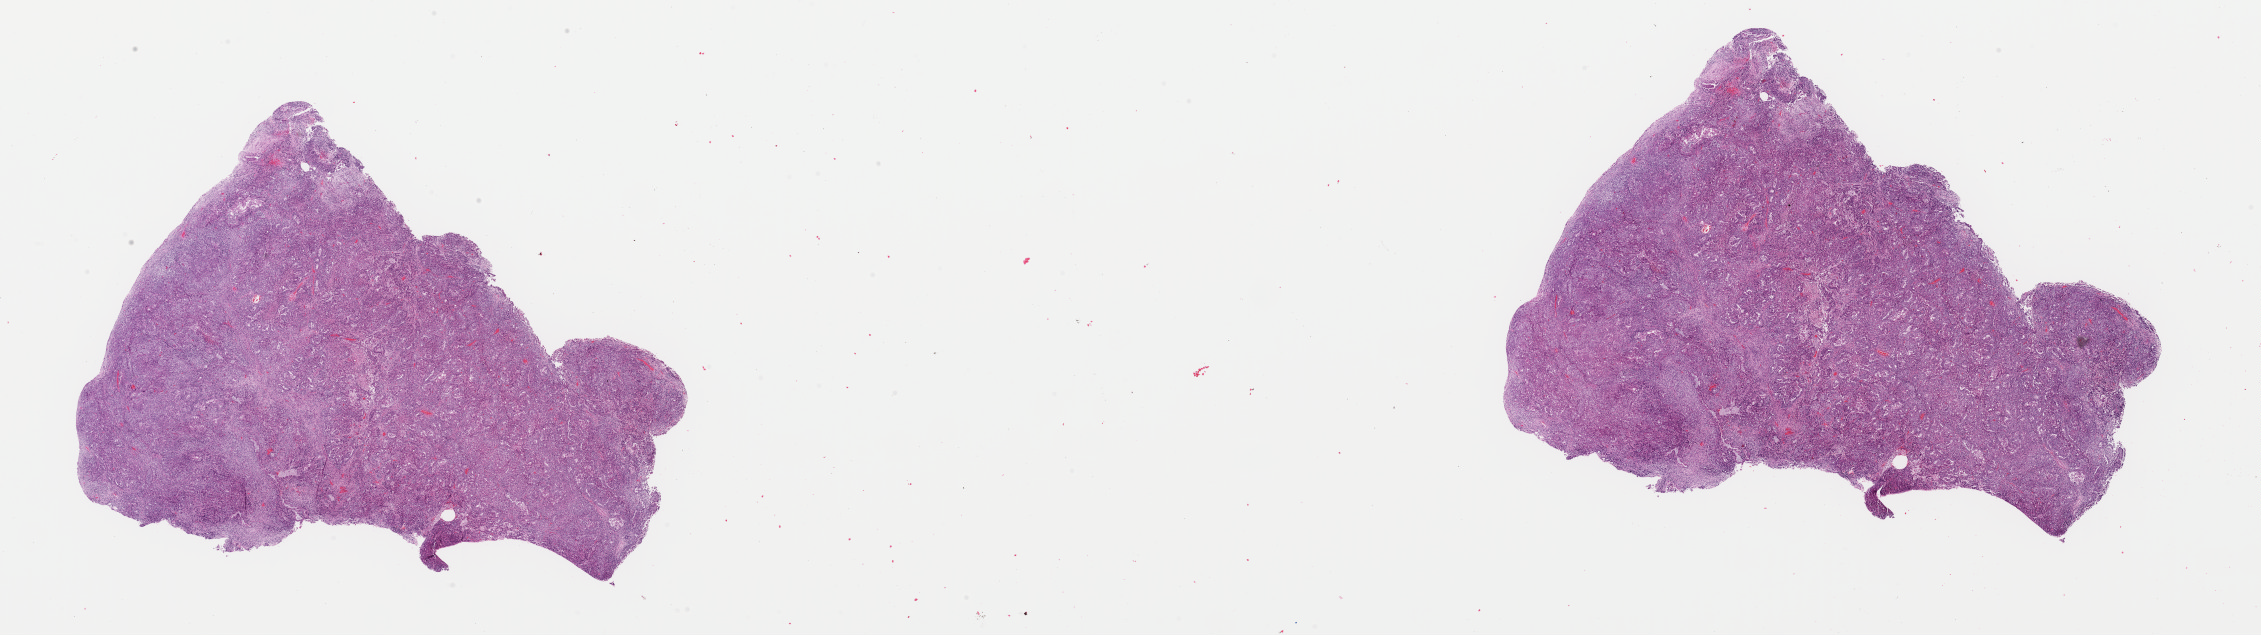
Whole-slide histology image, Hematoxylin and eosin (H&E) stained, whole scanned area (about 35.7 x 10.0 mm) shown as a low-resolution overview. FFPE section. Sample: primary tumour, uterus. Female patient; age at initial diagnosis 65 years.
• diagnosis: Mullerian mixed tumor
• FIGO stage: IA